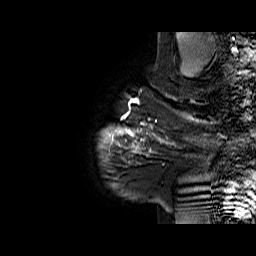
Breast MRI (dynamic contrast-enhanced), one sagittal slice; slice 59 of 60 in the series (ordered by position); dynamic contrast-enhanced series, time point 2 of 6 at this slice position (early post-contrast); 1.5 T; TE 6.1 ms, TR 32.9 ms; 256 × 256 image matrix. Female patient. From the clinical record (not read from this slice): setting: breast cancer imaged before/during neoadjuvant chemotherapy; receptor status: HER2-positive.
Structures marked on this image (semi-automatic segmentation, software-assisted and operator-edited):
- analysis volume of interest (the breast-tissue region the enhancement analysis was run in; not a lesion): box from (x=127, y=95) to (x=194, y=165) px
- tumour enhancement mask (voxels above the 100 % enhancement threshold inside the analysis volume of interest): (x=127, y=95)–(x=194, y=154)